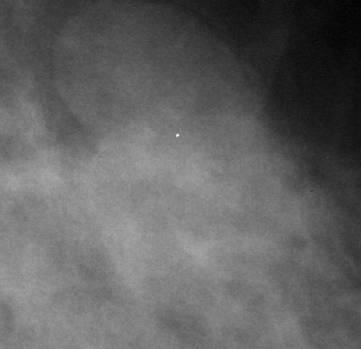
Cropped region of a digitized screen-film mammogram centred on a radiologist-marked abnormality; left breast; MLO view; BI-RADS breast density category 1 (scale 1–4).
Finding: mass, shape lobulated, margins obscured; BI-RADS assessment category 3; subtlety rating 5 on a 1 (subtle) to 5 (obvious) scale; pathology (as recorded): benign.